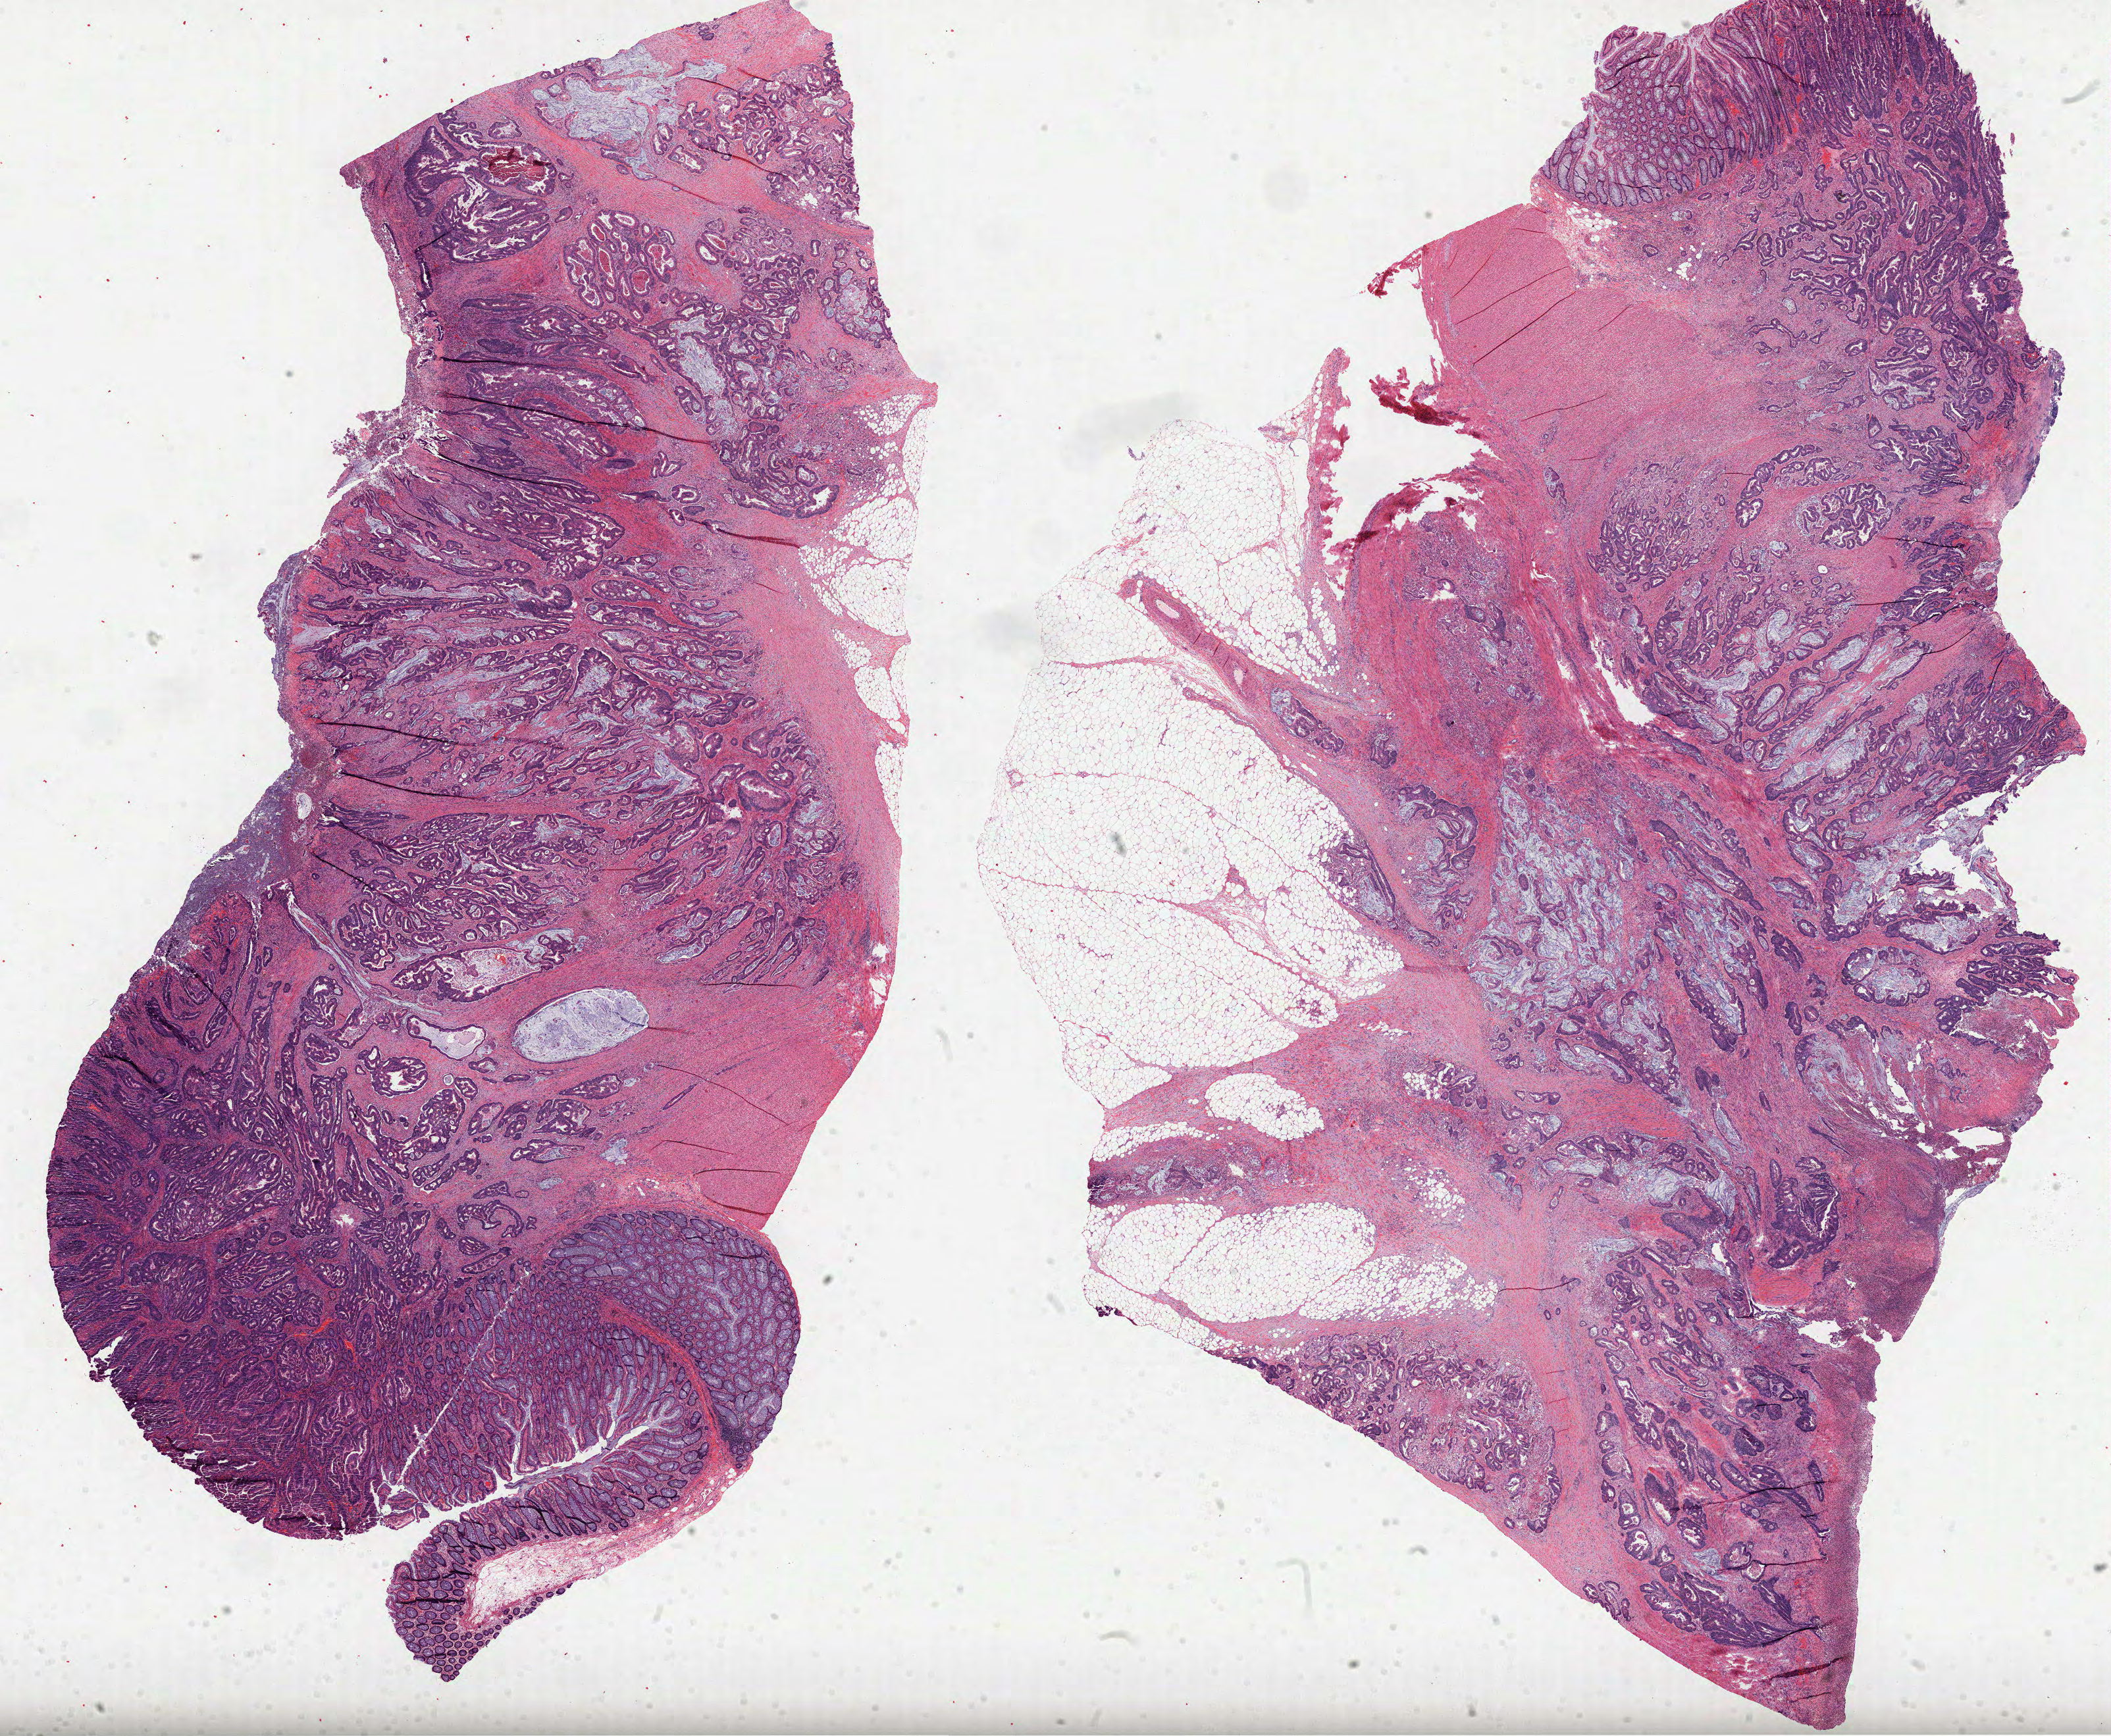
Whole-slide histology image, Hematoxylin and eosin (H&E) stained — shown as a low-resolution overview of the whole scanned area (about 25.9 x 21.3 mm, slide scanned at 40x), formalin-fixed paraffin-embedded (FFPE) diagnostic section, colon, primary tumour sample. Female, age 45 years at initial diagnosis.
AJCC pathologic stage: IV (6th edition). Pathologic diagnosis: Mucinous adenocarcinoma (sigmoid colon).